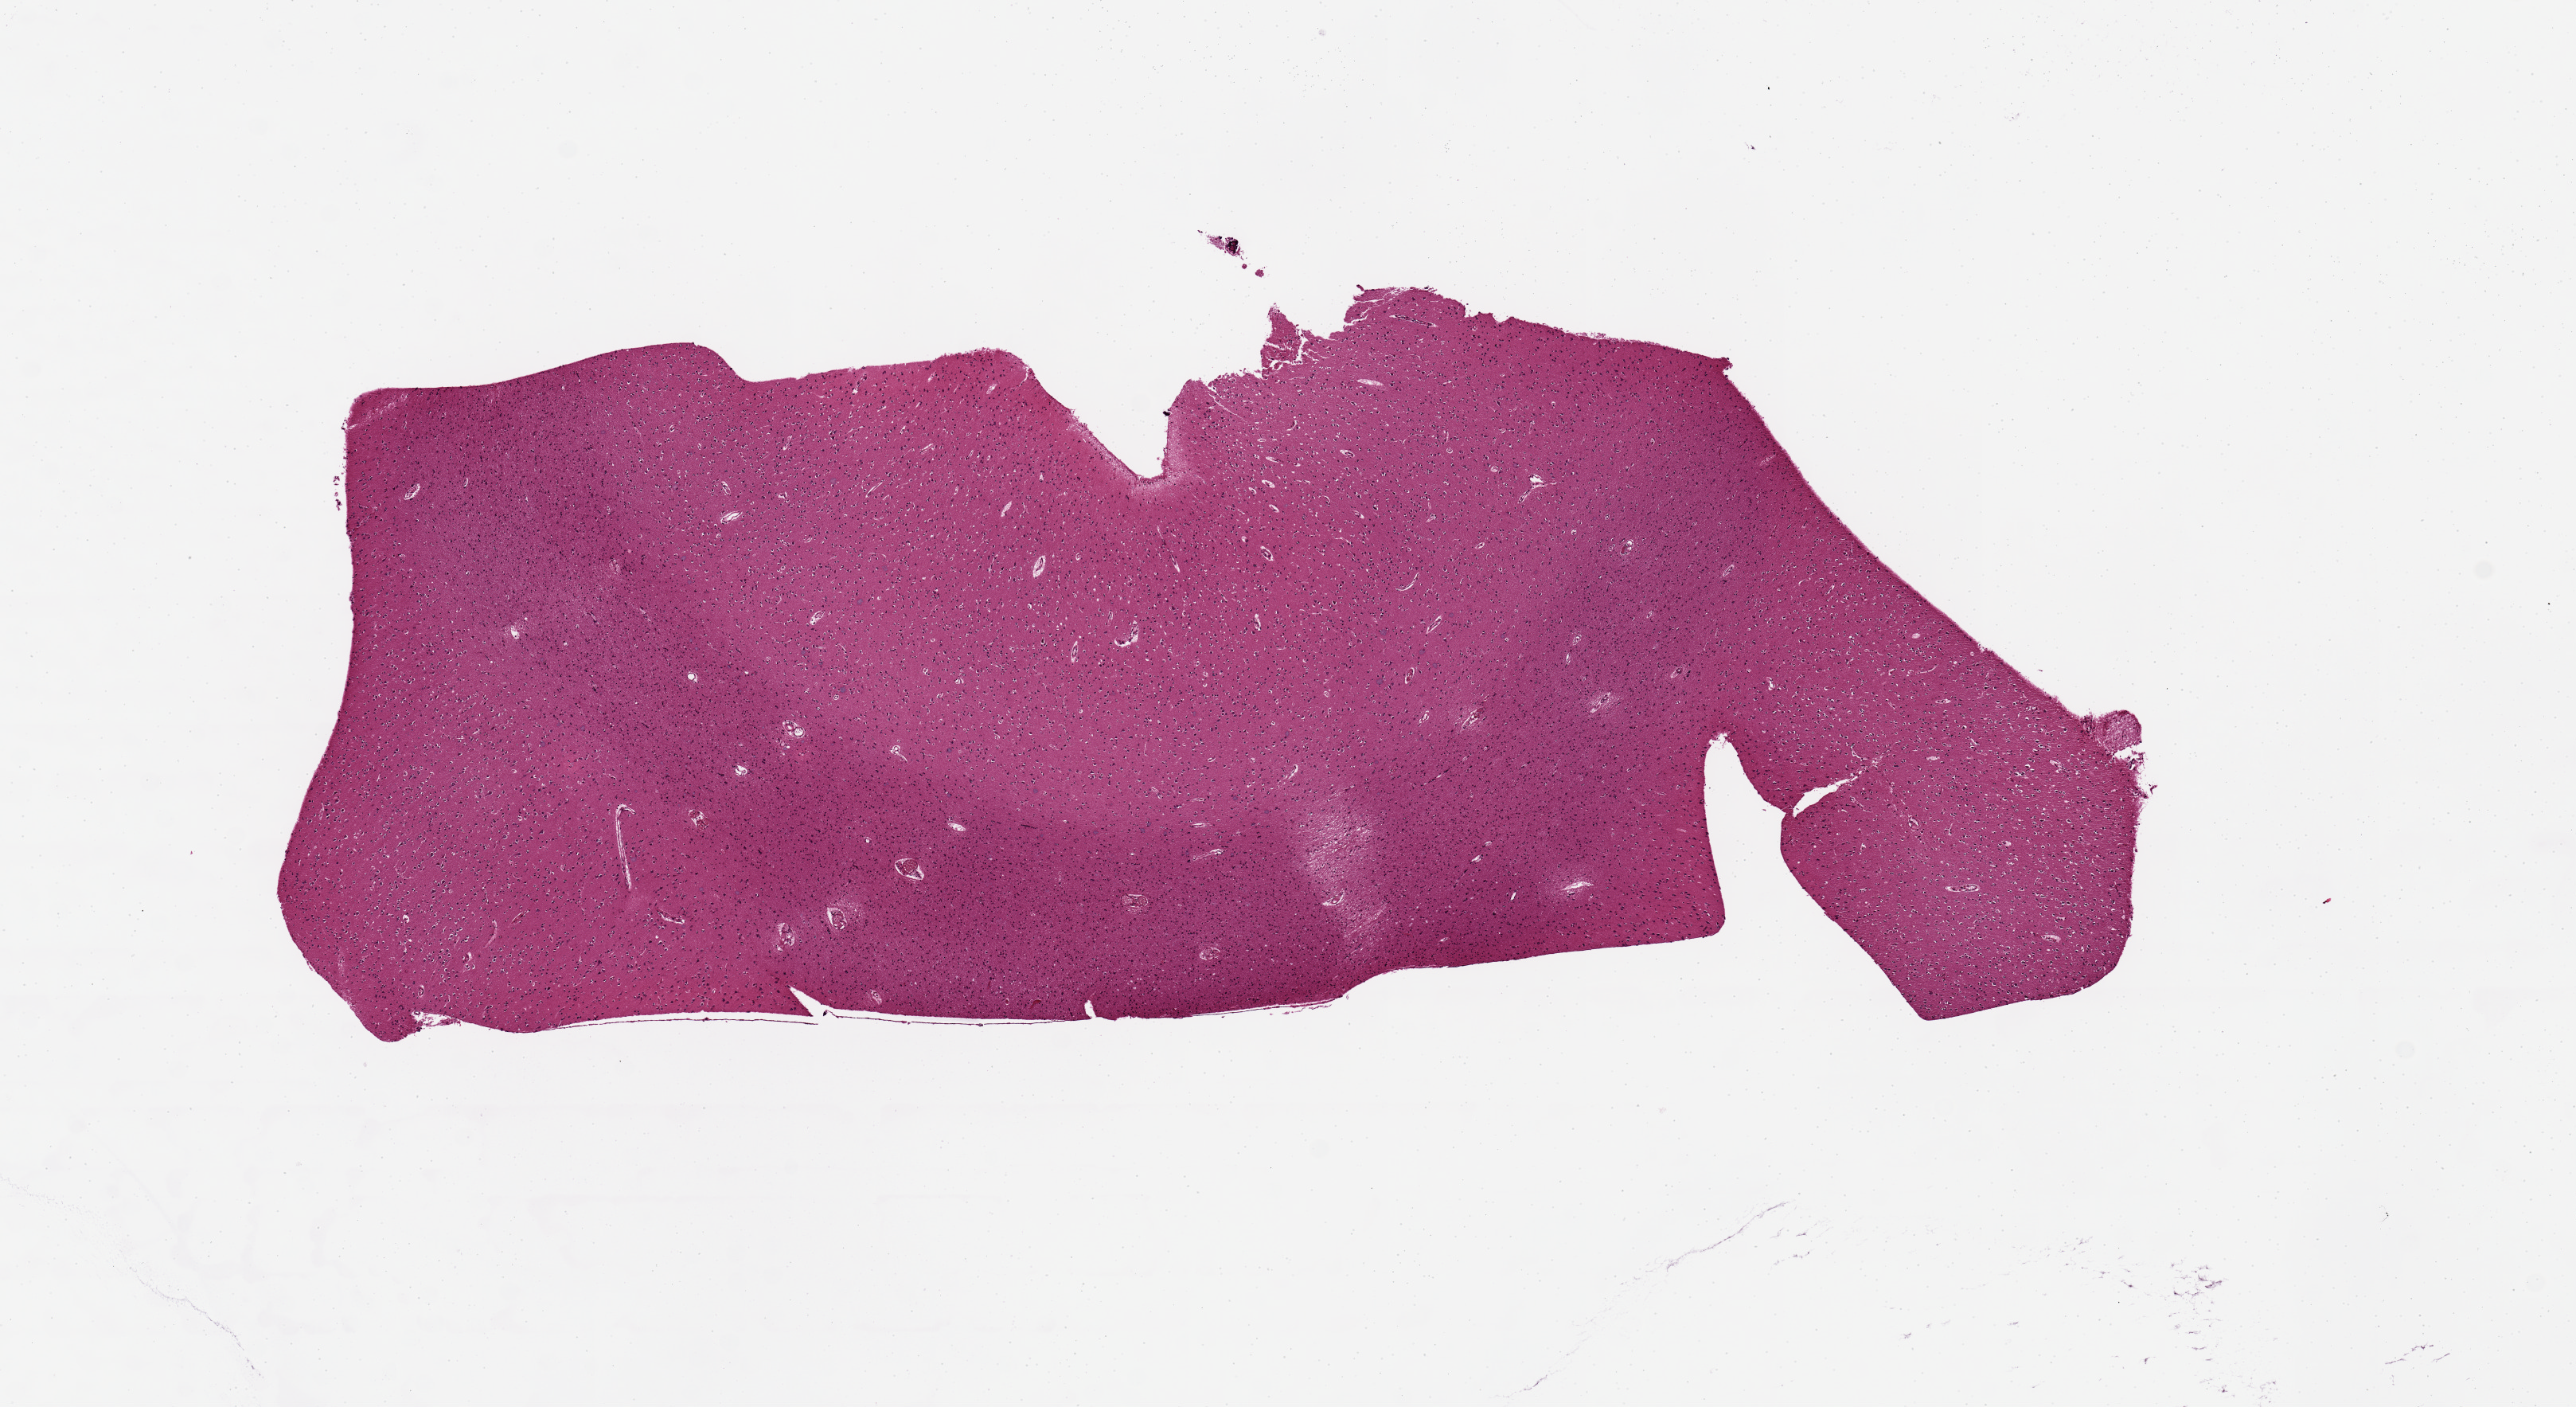
Digitized hematoxylin and eosin (H&E)-stained section, brightfield — whole scanned area (about 12.8 x 7.0 mm, slide scanned at 20x) shown as a low-resolution overview, PAXgene-fixed, paraffin-embedded tissue, section of cerebral cortex (target tissue), tissue donor sample. Donor sex: female.
- pathologist's review note for this sample: adequate for analysis